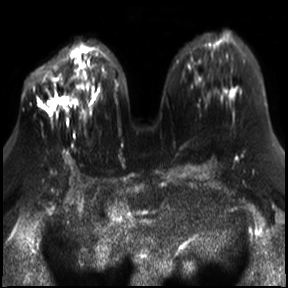
Breast MRI, one axial slice; slice 16 of 30 in the series (ordered by position); diffusion-weighted series; image 2 of 4 stored at this slice position (different b-values; order by instance number); 3 T; 288 × 288 image matrix, field of view 340 × 340 mm. Female patient.
Structures marked on this image (outlined manually by an expert reader):
- tumour on diffusion-weighted imaging: box from (x=47, y=95) to (x=70, y=112) px